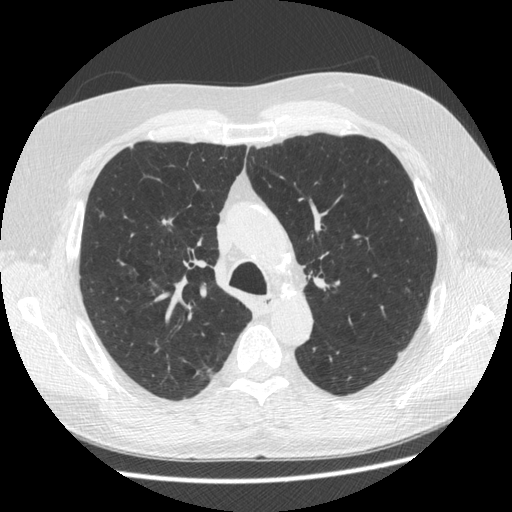
Axial slice from a low-dose chest CT screening exam, third annual screen, lung window (W 1500 / L -600 HU), standard (soft-tissue) reconstruction kernel (STANDARD), 512 × 512 image matrix, field of view 360 × 360 mm. Male, age 63 years at enrolment. Former smoker at enrolment.
Expert reader's lesion annotation, bounding box <150,208,183,237> (left, top, right, bottom; pixels). The screening reader recorded 2 non-calcified nodules or masses ≥4 mm on this exam (right upper lobe, left upper lobe); which of them this box marks is not recorded. Official screen result: positive, other. Later outcome: lung cancer diagnosed 342 days after this screen — adenocarcinoma, NOS, right upper lobe, stage IIA (AJCC 6th edition), 8 mm at pathology.